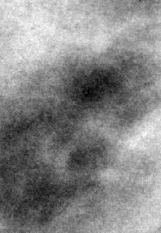
Crop from a digitized film mammogram around one marked abnormality, right breast, CC view, BI-RADS breast density category 3 (scale 1–4).
Finding: calcifications, morphology punctate / round and regular, distribution regional; BI-RADS assessment category 2; benign without callback (not worked up further).